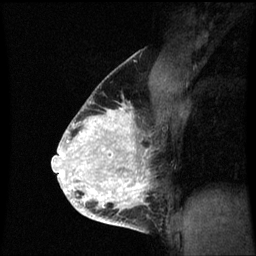
Breast MRI (dynamic contrast-enhanced), one sagittal slice; slice 42 of 60 in the series (ordered by position); dynamic contrast-enhanced series, image 2 of 3 at this slice position (ordered by acquisition); 1.5 T; TE 4.2 ms, TR 8.9 ms; 256 × 256 image matrix, field of view 200 × 200 mm. Female patient, age 35 years. From the clinical record (not read from this slice): setting: breast cancer imaged before/during neoadjuvant chemotherapy; receptor status: HR-positive, HER2-negative.
Structures marked on this image (semi-automatic segmentation, software-assisted and operator-edited):
- analysis volume of interest (the breast-tissue region the enhancement analysis was run in; not a lesion): bounding box (x1, y1, x2, y2) in pixels: (66, 100, 159, 215)
- tumour enhancement mask (voxels above the 70 % enhancement threshold inside the analysis volume of interest): (66, 102, 150, 213)